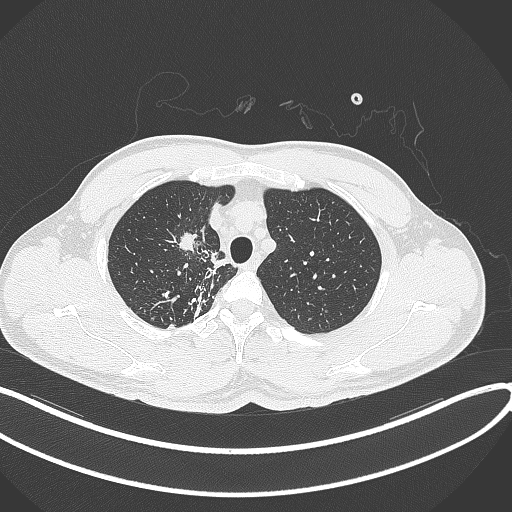
Chest CT, one axial slice; 120 kVp; lung window (W 1500 / L -600 HU); 1 mm slice thickness; 512 × 512 image matrix. Male patient, age 48 years. From the clinical record (not read from this slice): clinical TNM (as recorded): T1c N1 M1.
Structures marked on this image (bounding box drawn by a radiologist):
- lung tumour (recorded histology: adenocarcinoma): bounding box (x1, y1, x2, y2) in pixels: (173, 229, 201, 257)